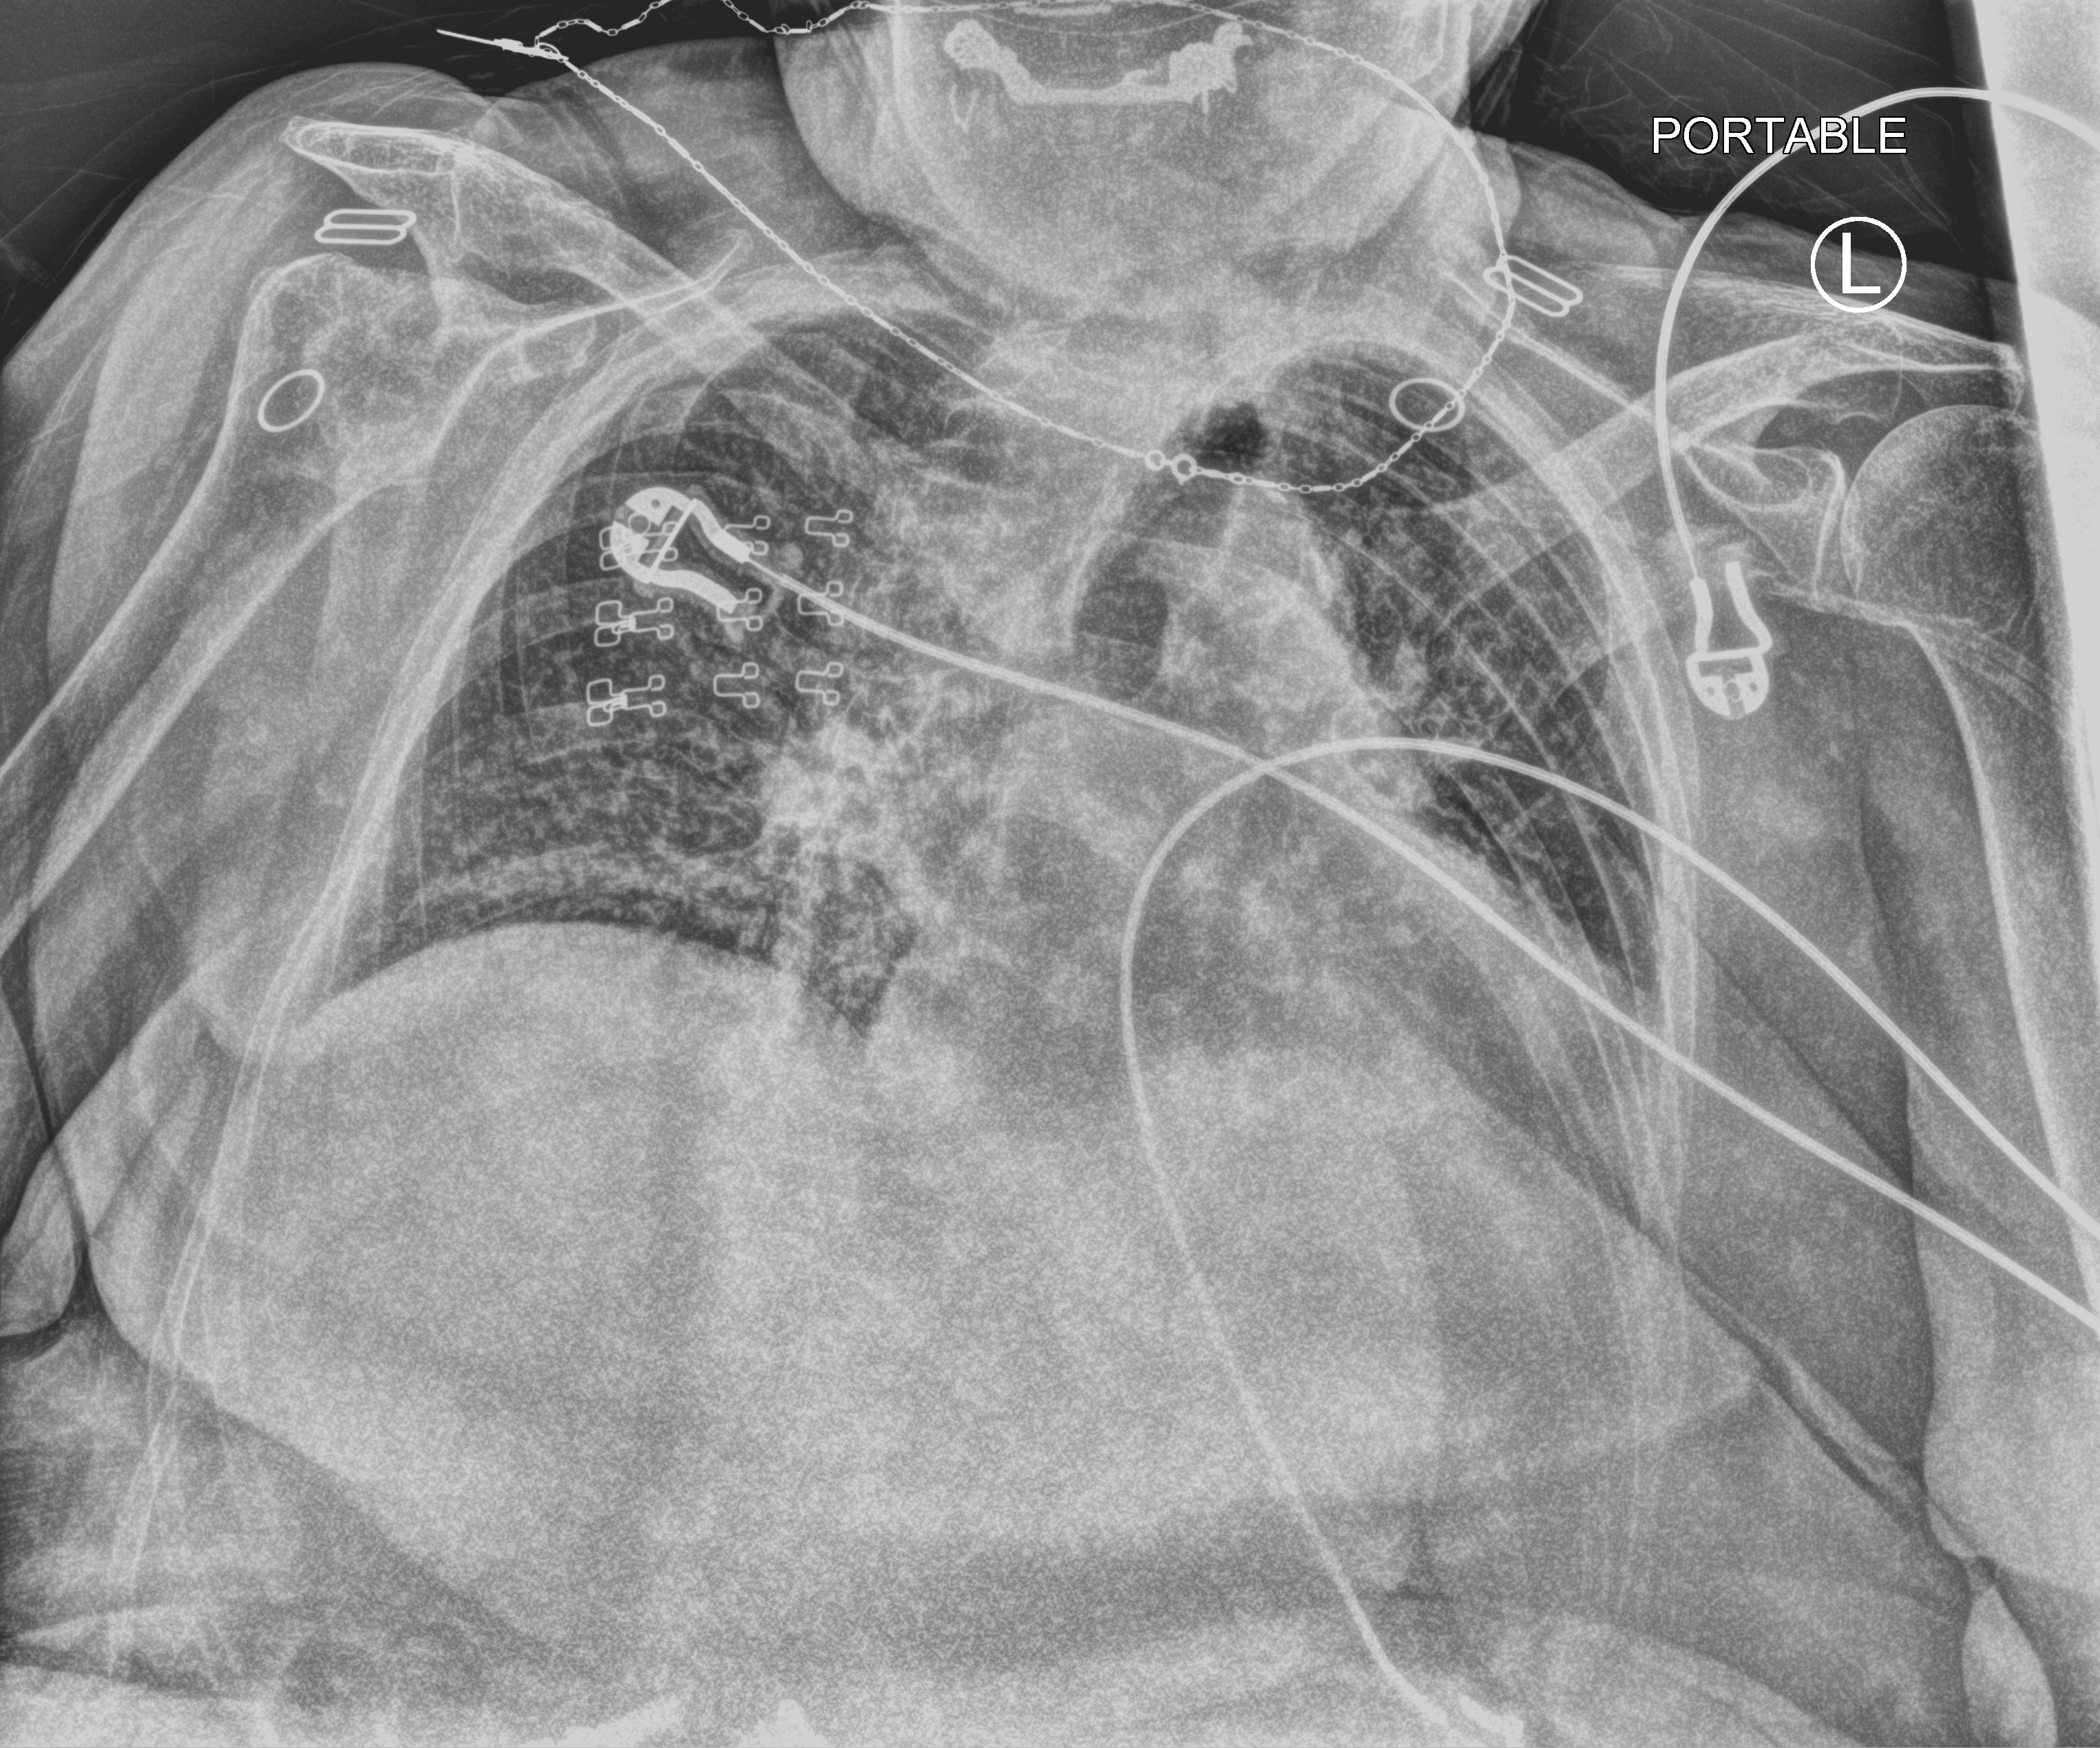
Portable chest radiograph; anteroposterior (AP) projection. Patient hospitalised with COVID-19; female, aged 75–90 years.
Admission-level facts for this patient (not findings on this image; timing relative to this image not recorded): smoking status (admission record): former; chronic kidney disease (admission record): yes.